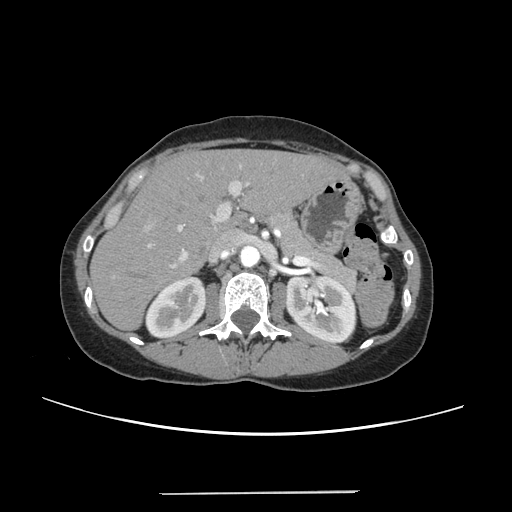
Contrast-enhanced abdominal CT, one axial slice; position 147 of 240 along the scan axis; intravenous contrast given; soft-tissue window (W 400 / L 40 HU); 1.25 mm slice thickness; 512 × 512 image matrix, field of view 371 × 371 mm. Female patient, age 60 years. From the clinical record (not read from this slice): diagnosis: colorectal cancer liver metastases, imaged before liver resection; multiple liver metastases: no.
Annotated regions visible in this slice (outlined manually by an expert reader):
- liver: box from (x=93, y=150) to (x=344, y=328) px
- planned liver remnant (the part of the liver to remain after resection): (x=93, y=150)–(x=343, y=328)
- portal vein (with intrahepatic branches): (x=144, y=164)–(x=250, y=267)